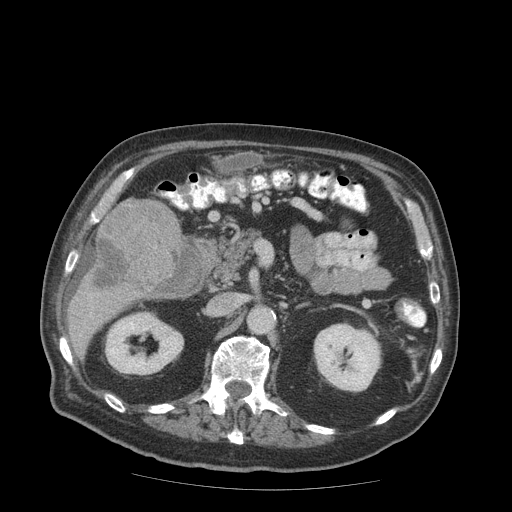
Contrast-enhanced abdominal CT (liver protocol), one axial slice; reconstruction kernel STANDARD; soft-tissue window (W 400 / L 40 HU); 2.5 mm slice thickness; 512 × 512 image matrix, field of view 420 × 420 mm. From the clinical record (not read from this slice): diagnosis: hepatocellular carcinoma (patient treated with transarterial chemoembolisation; whether this scan precedes or follows treatment is not stated here); TNM stage (as recorded): Stage-IIIB; Child-Pugh class: A; tumour nodularity: multinodular.
Outlined on this slice (semi-automatic segmentation, software-assisted and operator-edited):
- liver parenchyma outside the tumour (the mass and vessels are separate outlines, so this box may not span the whole liver): box from (x=68, y=198) to (x=186, y=350) px
- mass: (x=93, y=198)–(x=183, y=301)